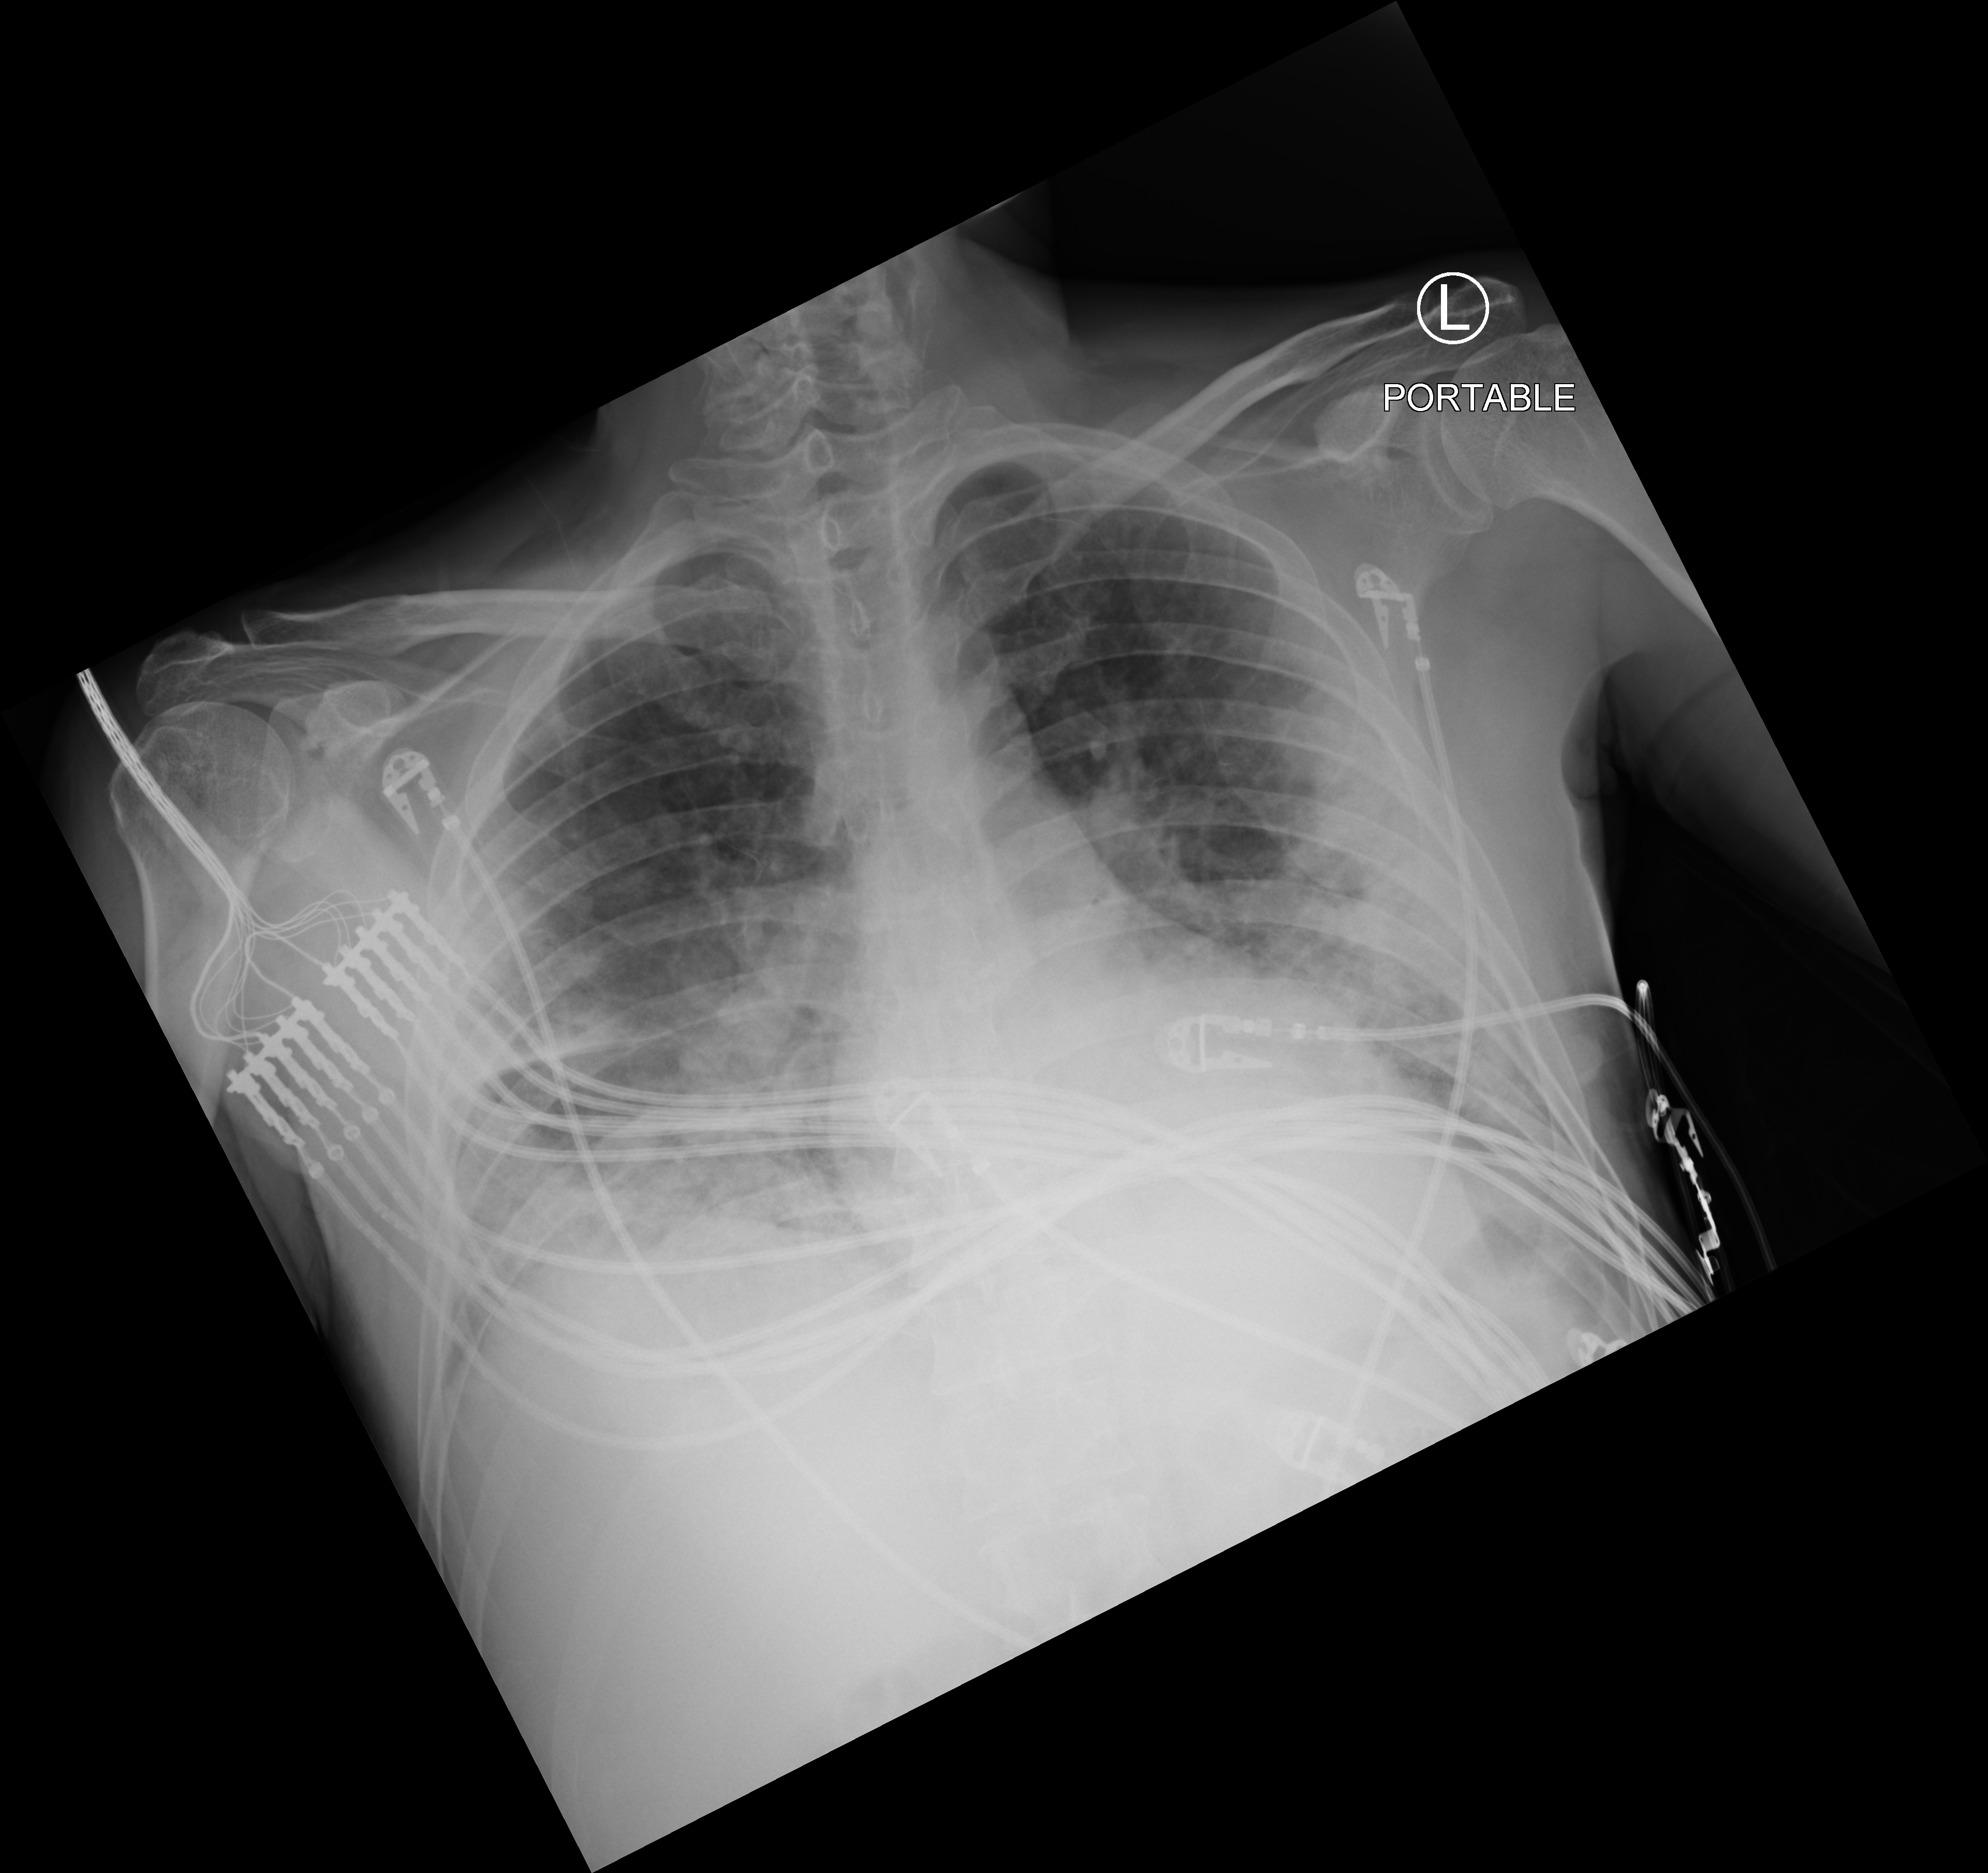
Bedside chest radiograph (computed radiography); anteroposterior (AP) projection. Patient hospitalised with COVID-19; male, aged 18–59 years.
Hospital-stay facts (about this admission, not read from this image; timing relative to this image not recorded): chronic kidney disease (admission record): no; COPD (admission record): no; mechanically ventilated during this hospital stay: yes.